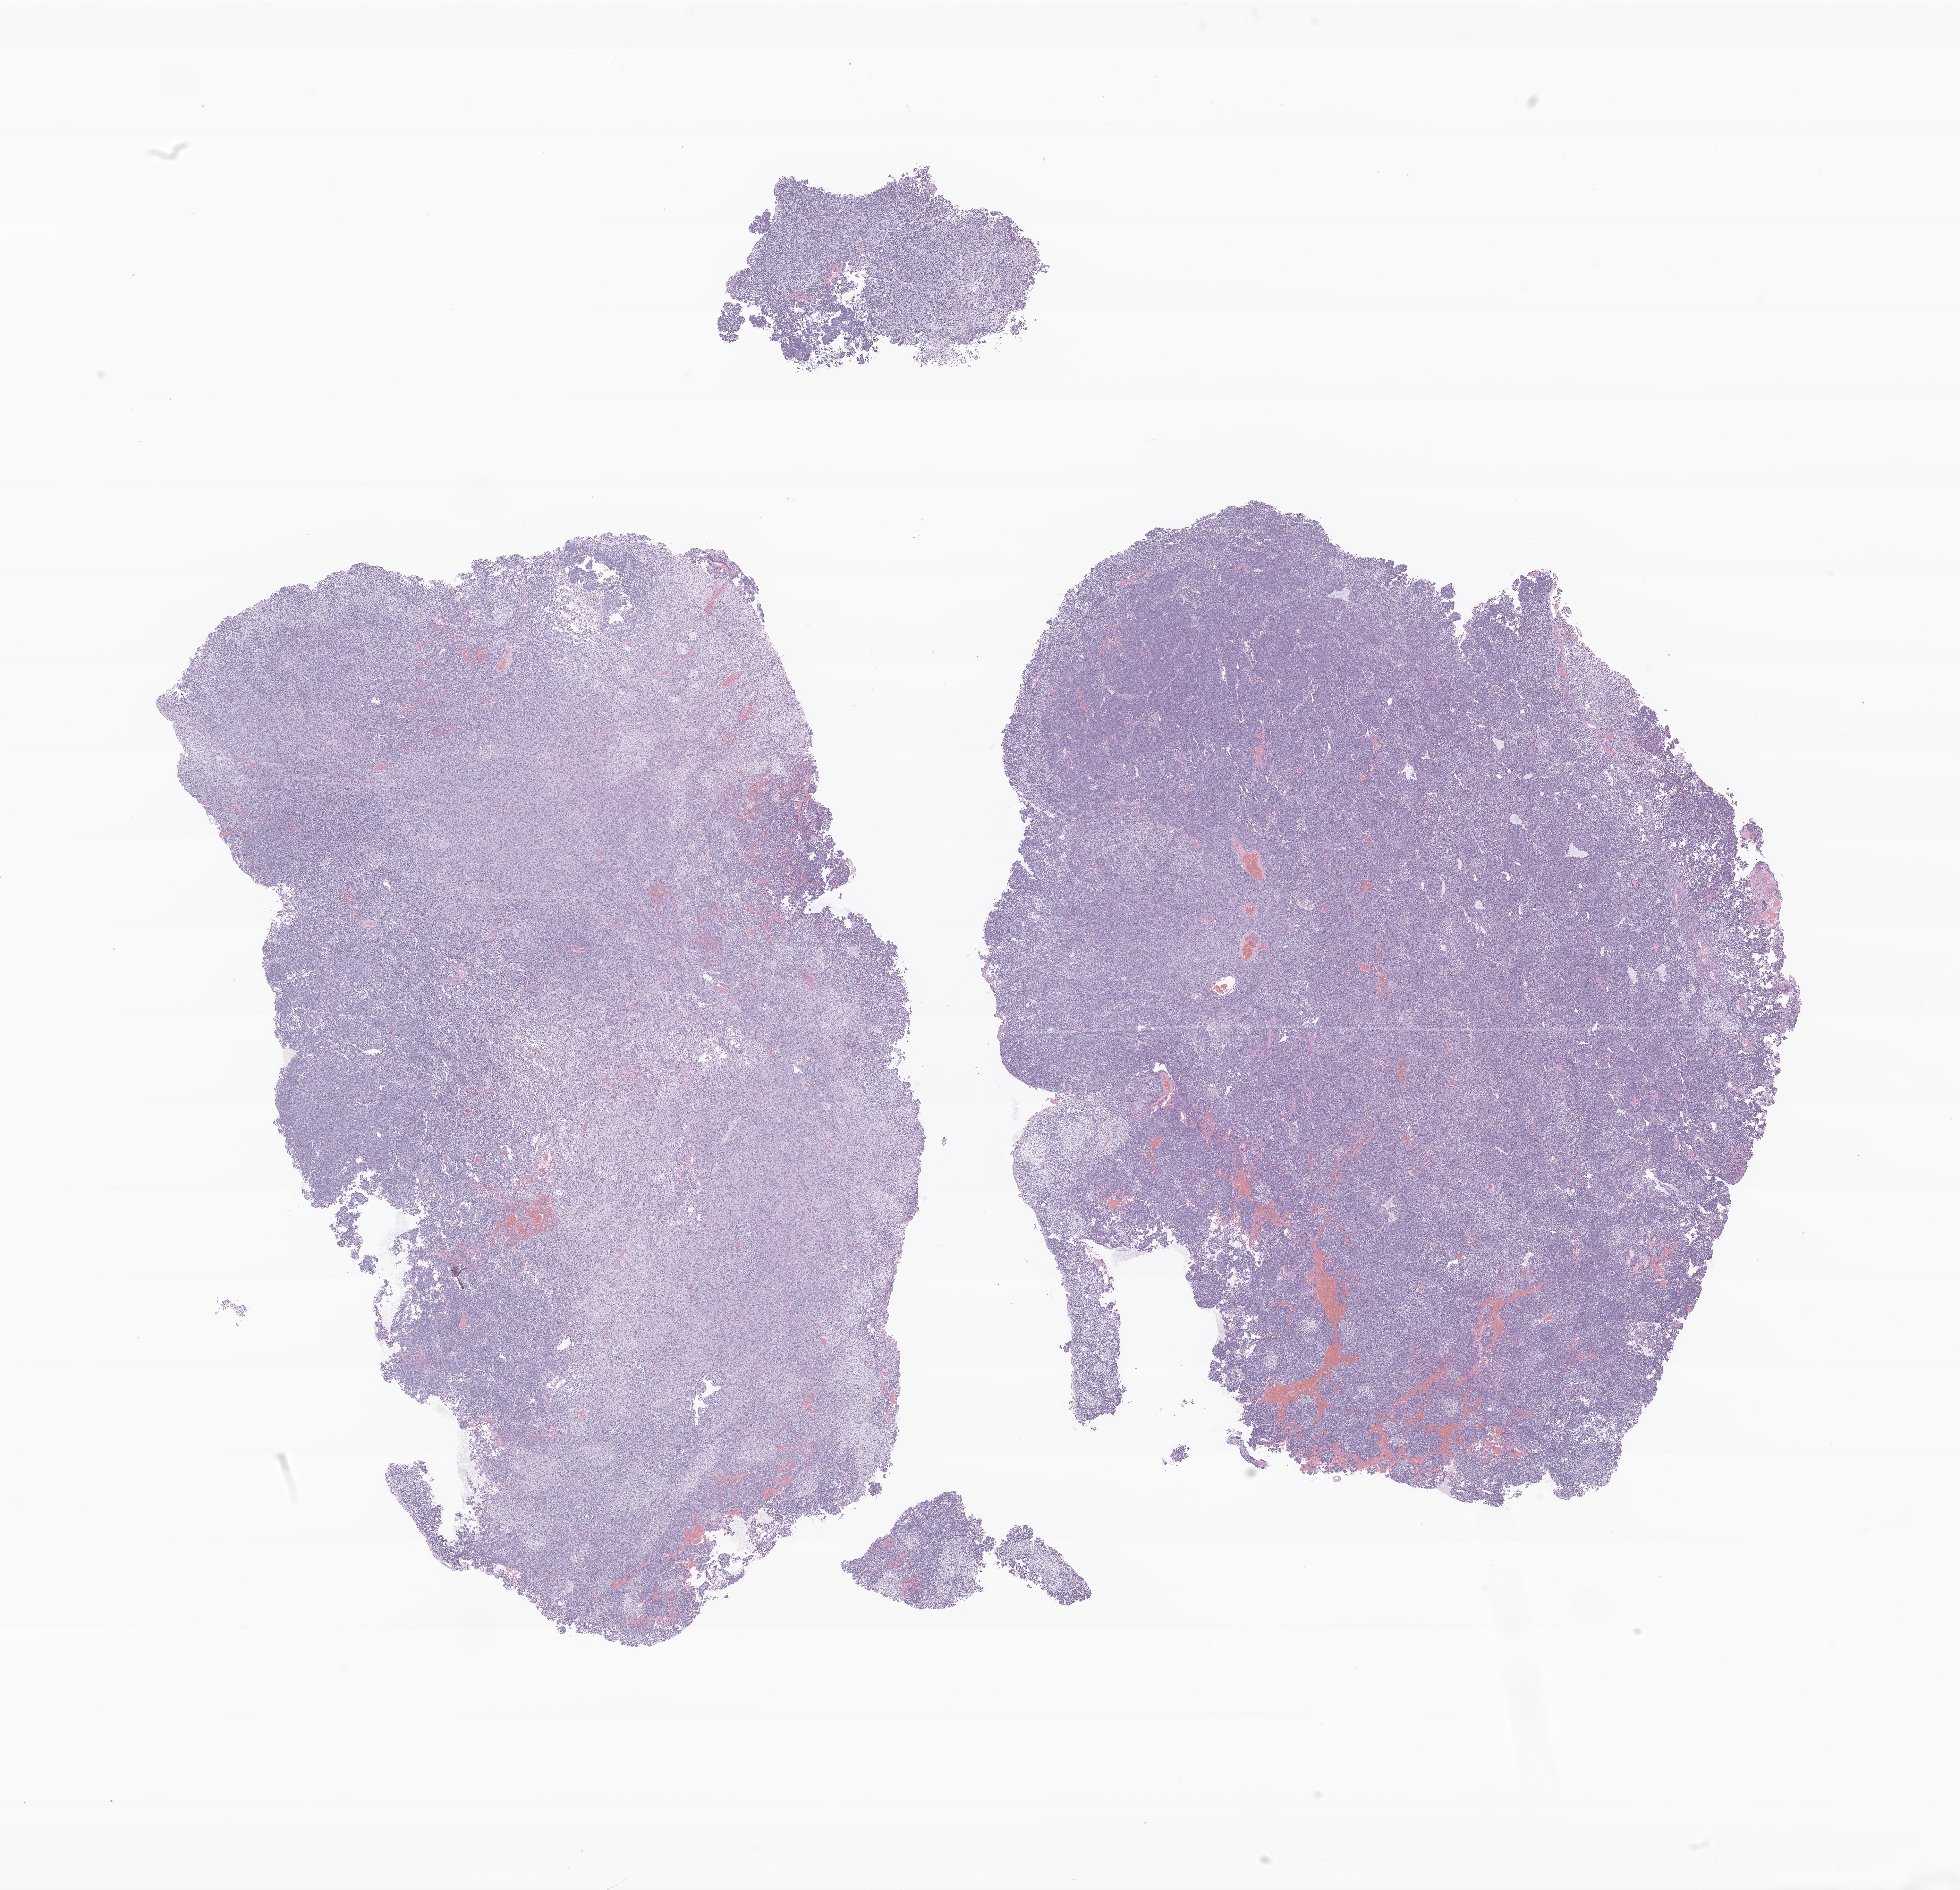
Whole-slide image, H&E stain of tumor tissue from the brain — a low-resolution overview of the entire scanned area, about 23.7 x 22.9 mm; formalin-fixed paraffin-embedded section. Patient female; age 150 months.
Diagnosis: Medulloblastoma, NOS.